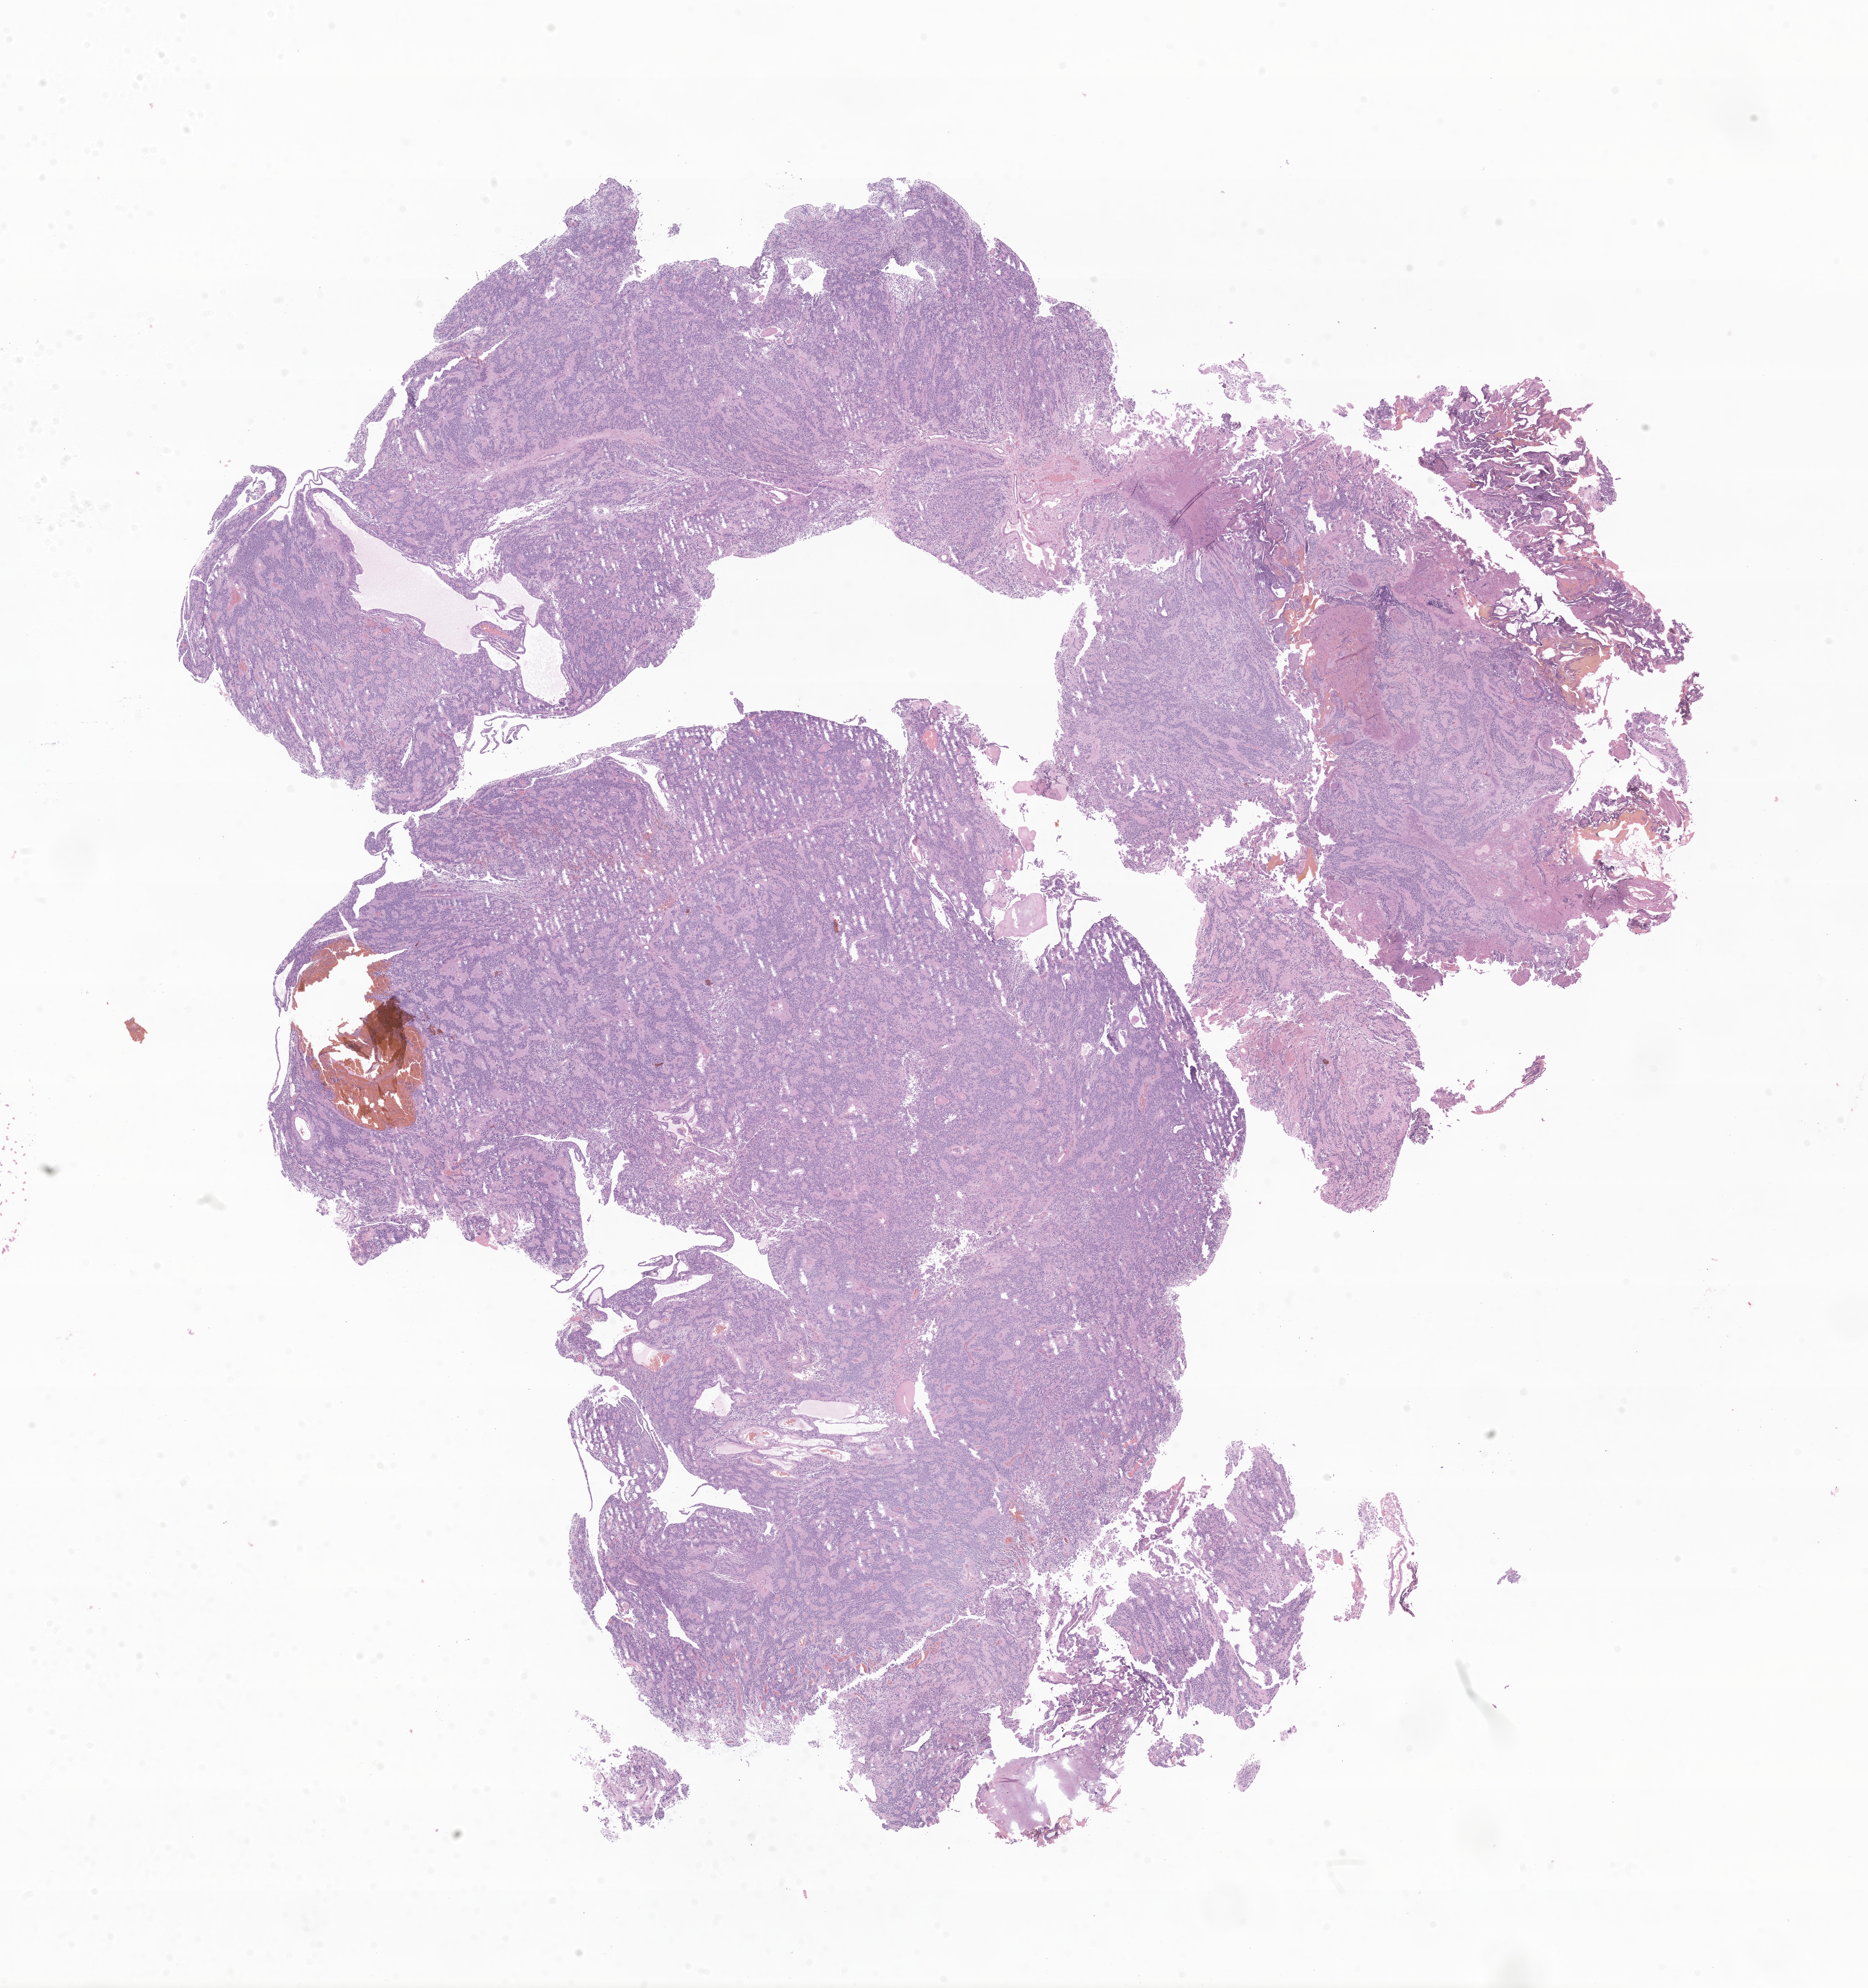
Hematoxylin and eosin (H&E) whole-slide image of tumor tissue from the brain — a low-resolution overview of the entire scanned area, about 19.8 x 21.1 mm; formalin-fixed paraffin-embedded section. Female patient, age 194 months (16 years 2 months).
Recorded diagnosis: Glioma, malignant.